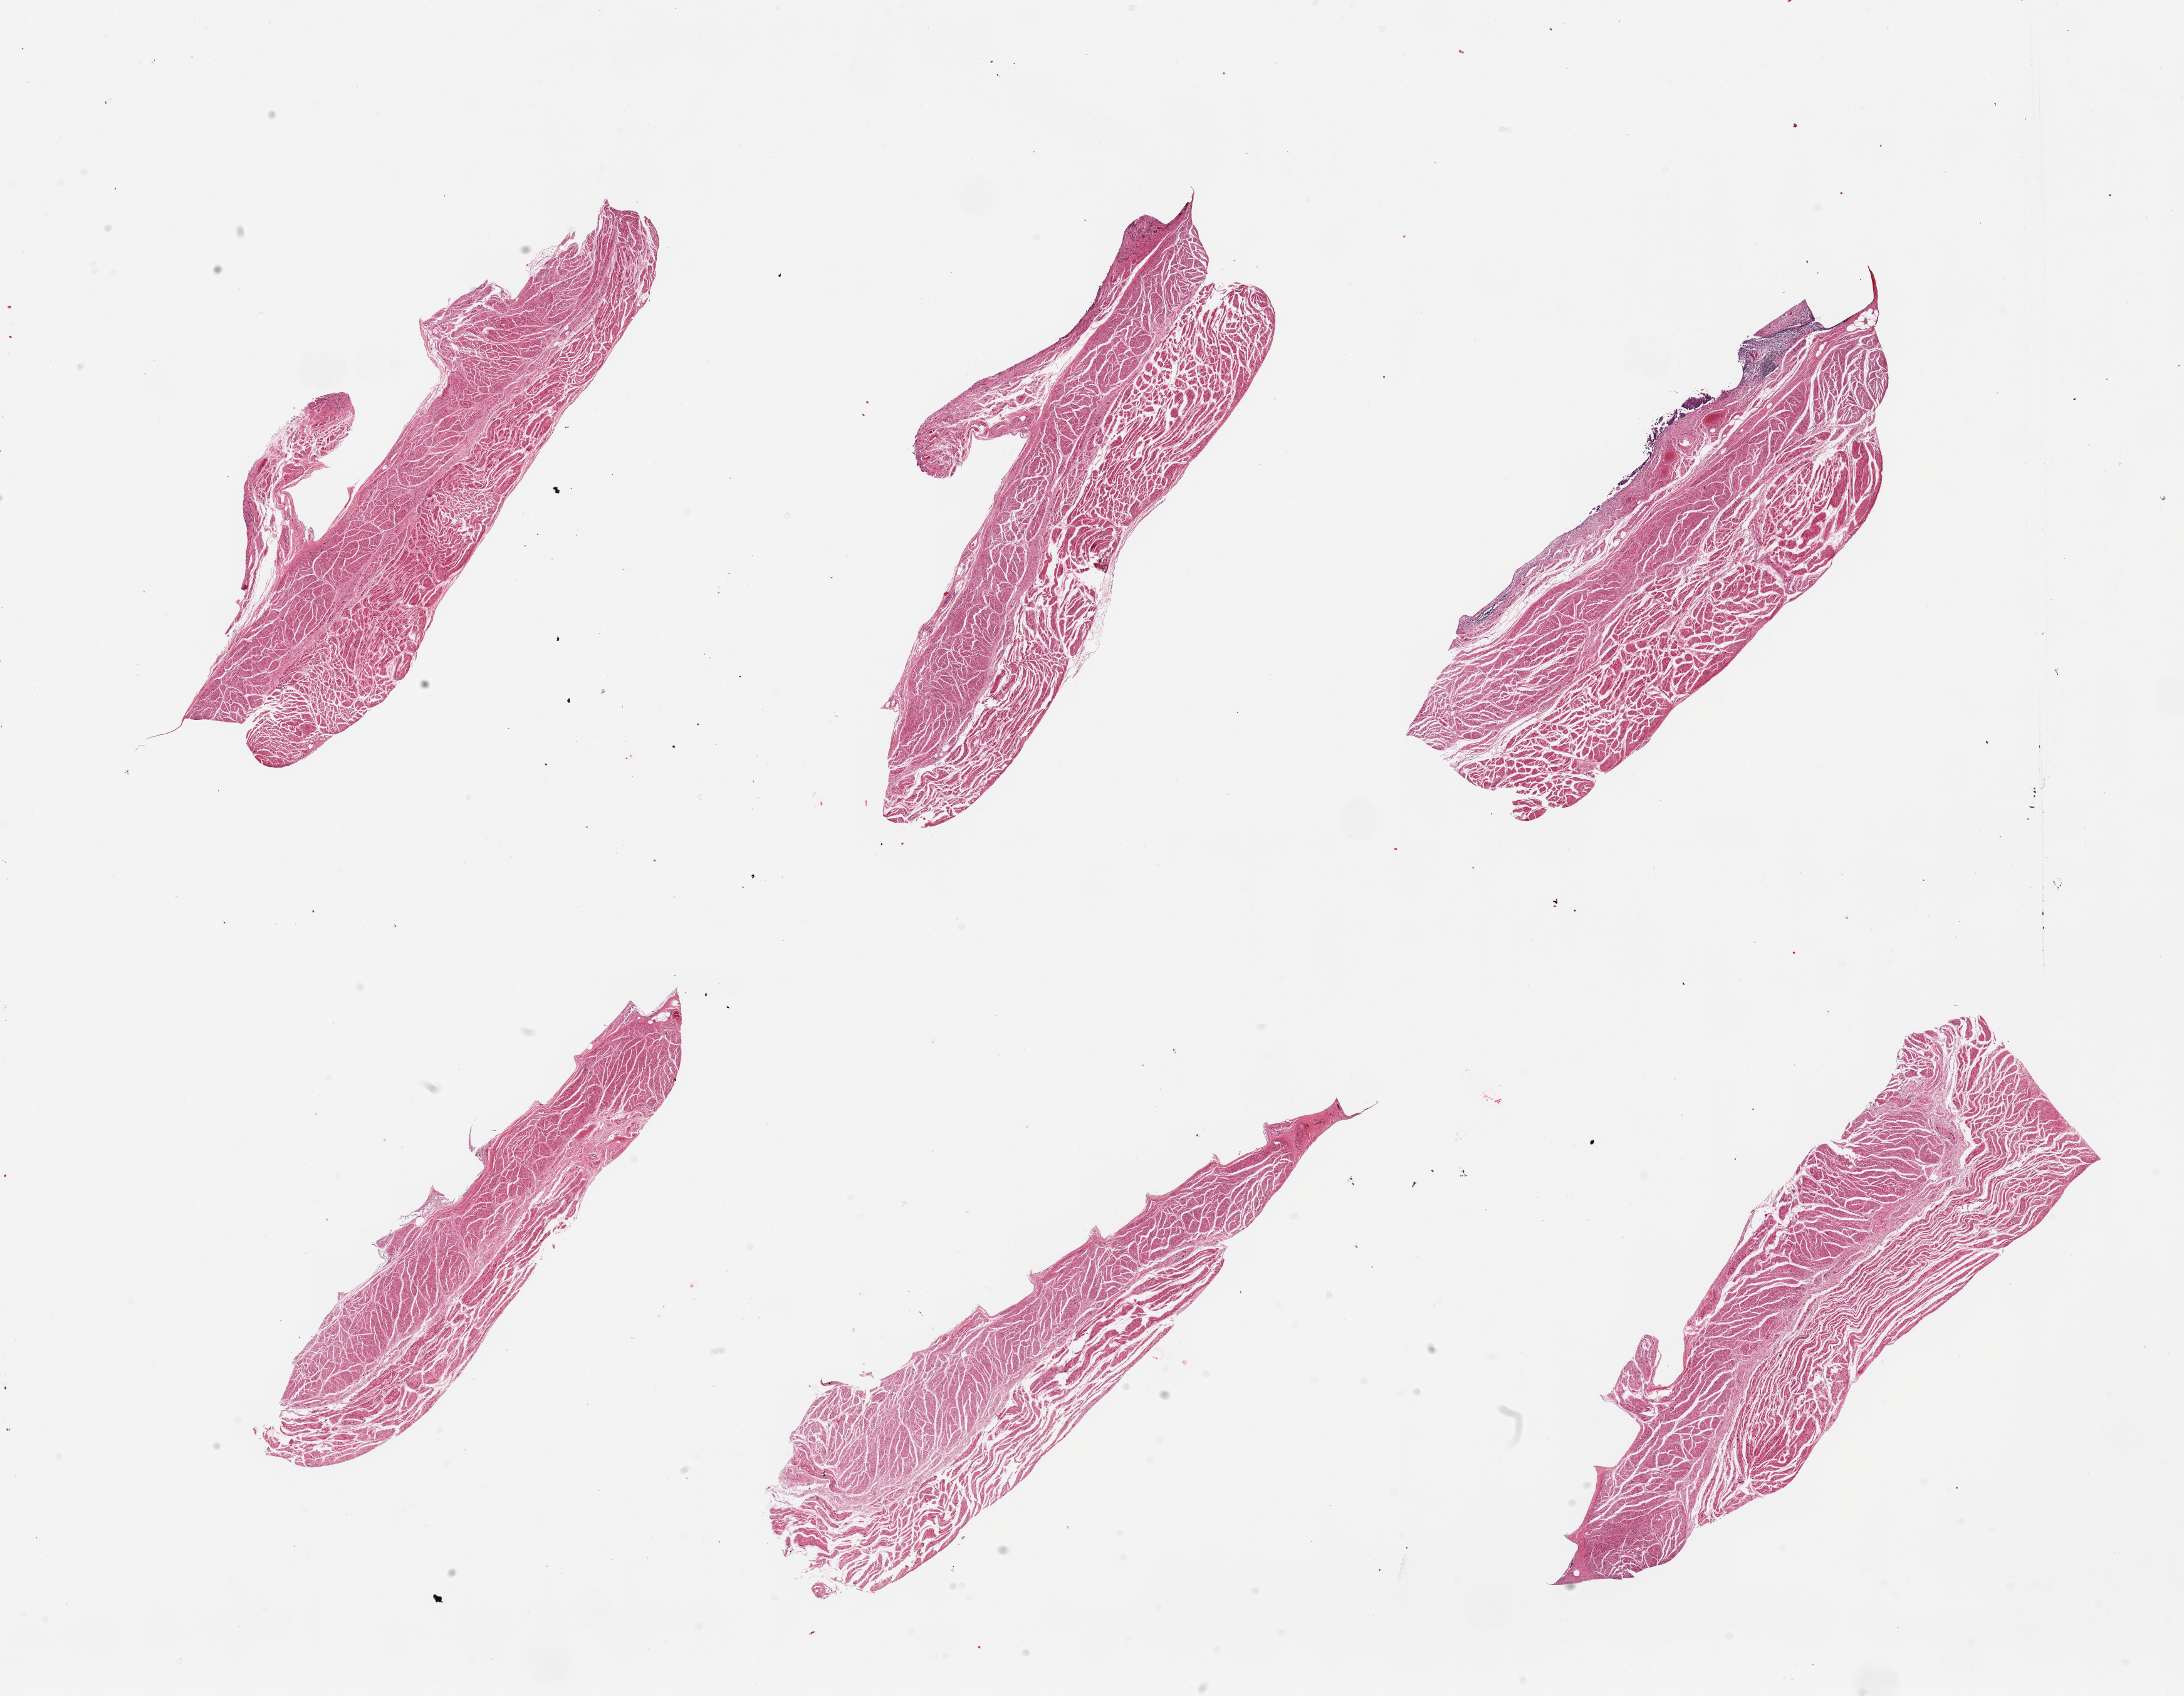
Digitized H&E-stained section — whole scanned area (about 27.6 x 21.4 mm, slide scanned at 20x) shown as a low-resolution overview. PAXgene-fixed, paraffin-embedded tissue. Target tissue: gastroesophageal junction. Donor tissue sample. Donor sex: male.
Review note (as recorded): 6 pieces, all target muscularis.